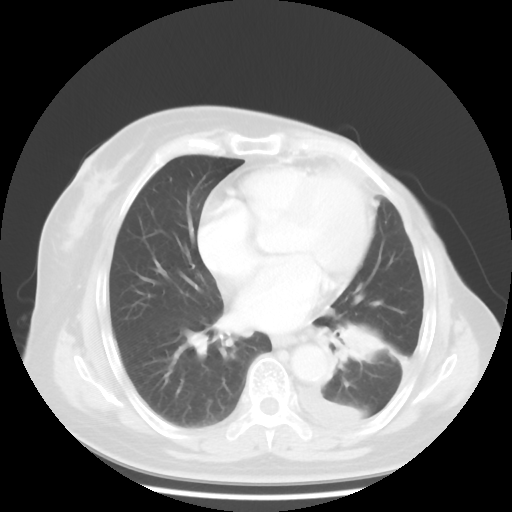
Chest CT, one axial slice; position 20 of 48 along the scan axis; reconstruction kernel STANDARD; 120 kVp; lung window (W 1500 / L -600 HU); 512 × 512 image matrix, field of view 360 × 360 mm. Female patient, age 63 years. Case-level facts recorded for this patient, not image findings: clinical TNM (as recorded): T2 N0 M1.
Annotated regions visible in this slice (bounding box drawn by a radiologist):
- lung tumour (recorded histology: adenocarcinoma): box from (x=322, y=303) to (x=393, y=377) px